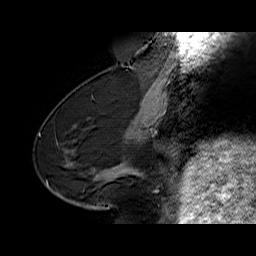
Breast MRI (dynamic contrast-enhanced), one sagittal slice. Position 27 of 60 along the scan axis. Dynamic contrast-enhanced series, time point 2 of 6 at this slice position (early post-contrast). 1.5 T. TE 6.4 ms, TR 32.9 ms. 4 mm slice thickness. 256 × 256 image matrix, field of view 200 × 200 mm. Female patient. From the clinical record (not read from this slice): setting: breast cancer imaged before/during neoadjuvant chemotherapy; receptor status: HR-positive, HER2-negative.
Structures marked on this image (semi-automatic segmentation, software-assisted and operator-edited):
- analysis volume of interest (the breast-tissue region the enhancement analysis was run in; not a lesion): bounding box (x1, y1, x2, y2) in pixels: (68, 154, 129, 203)
- tumour enhancement mask (voxels above the 100 % enhancement threshold inside the analysis volume of interest): (112, 169, 114, 171)